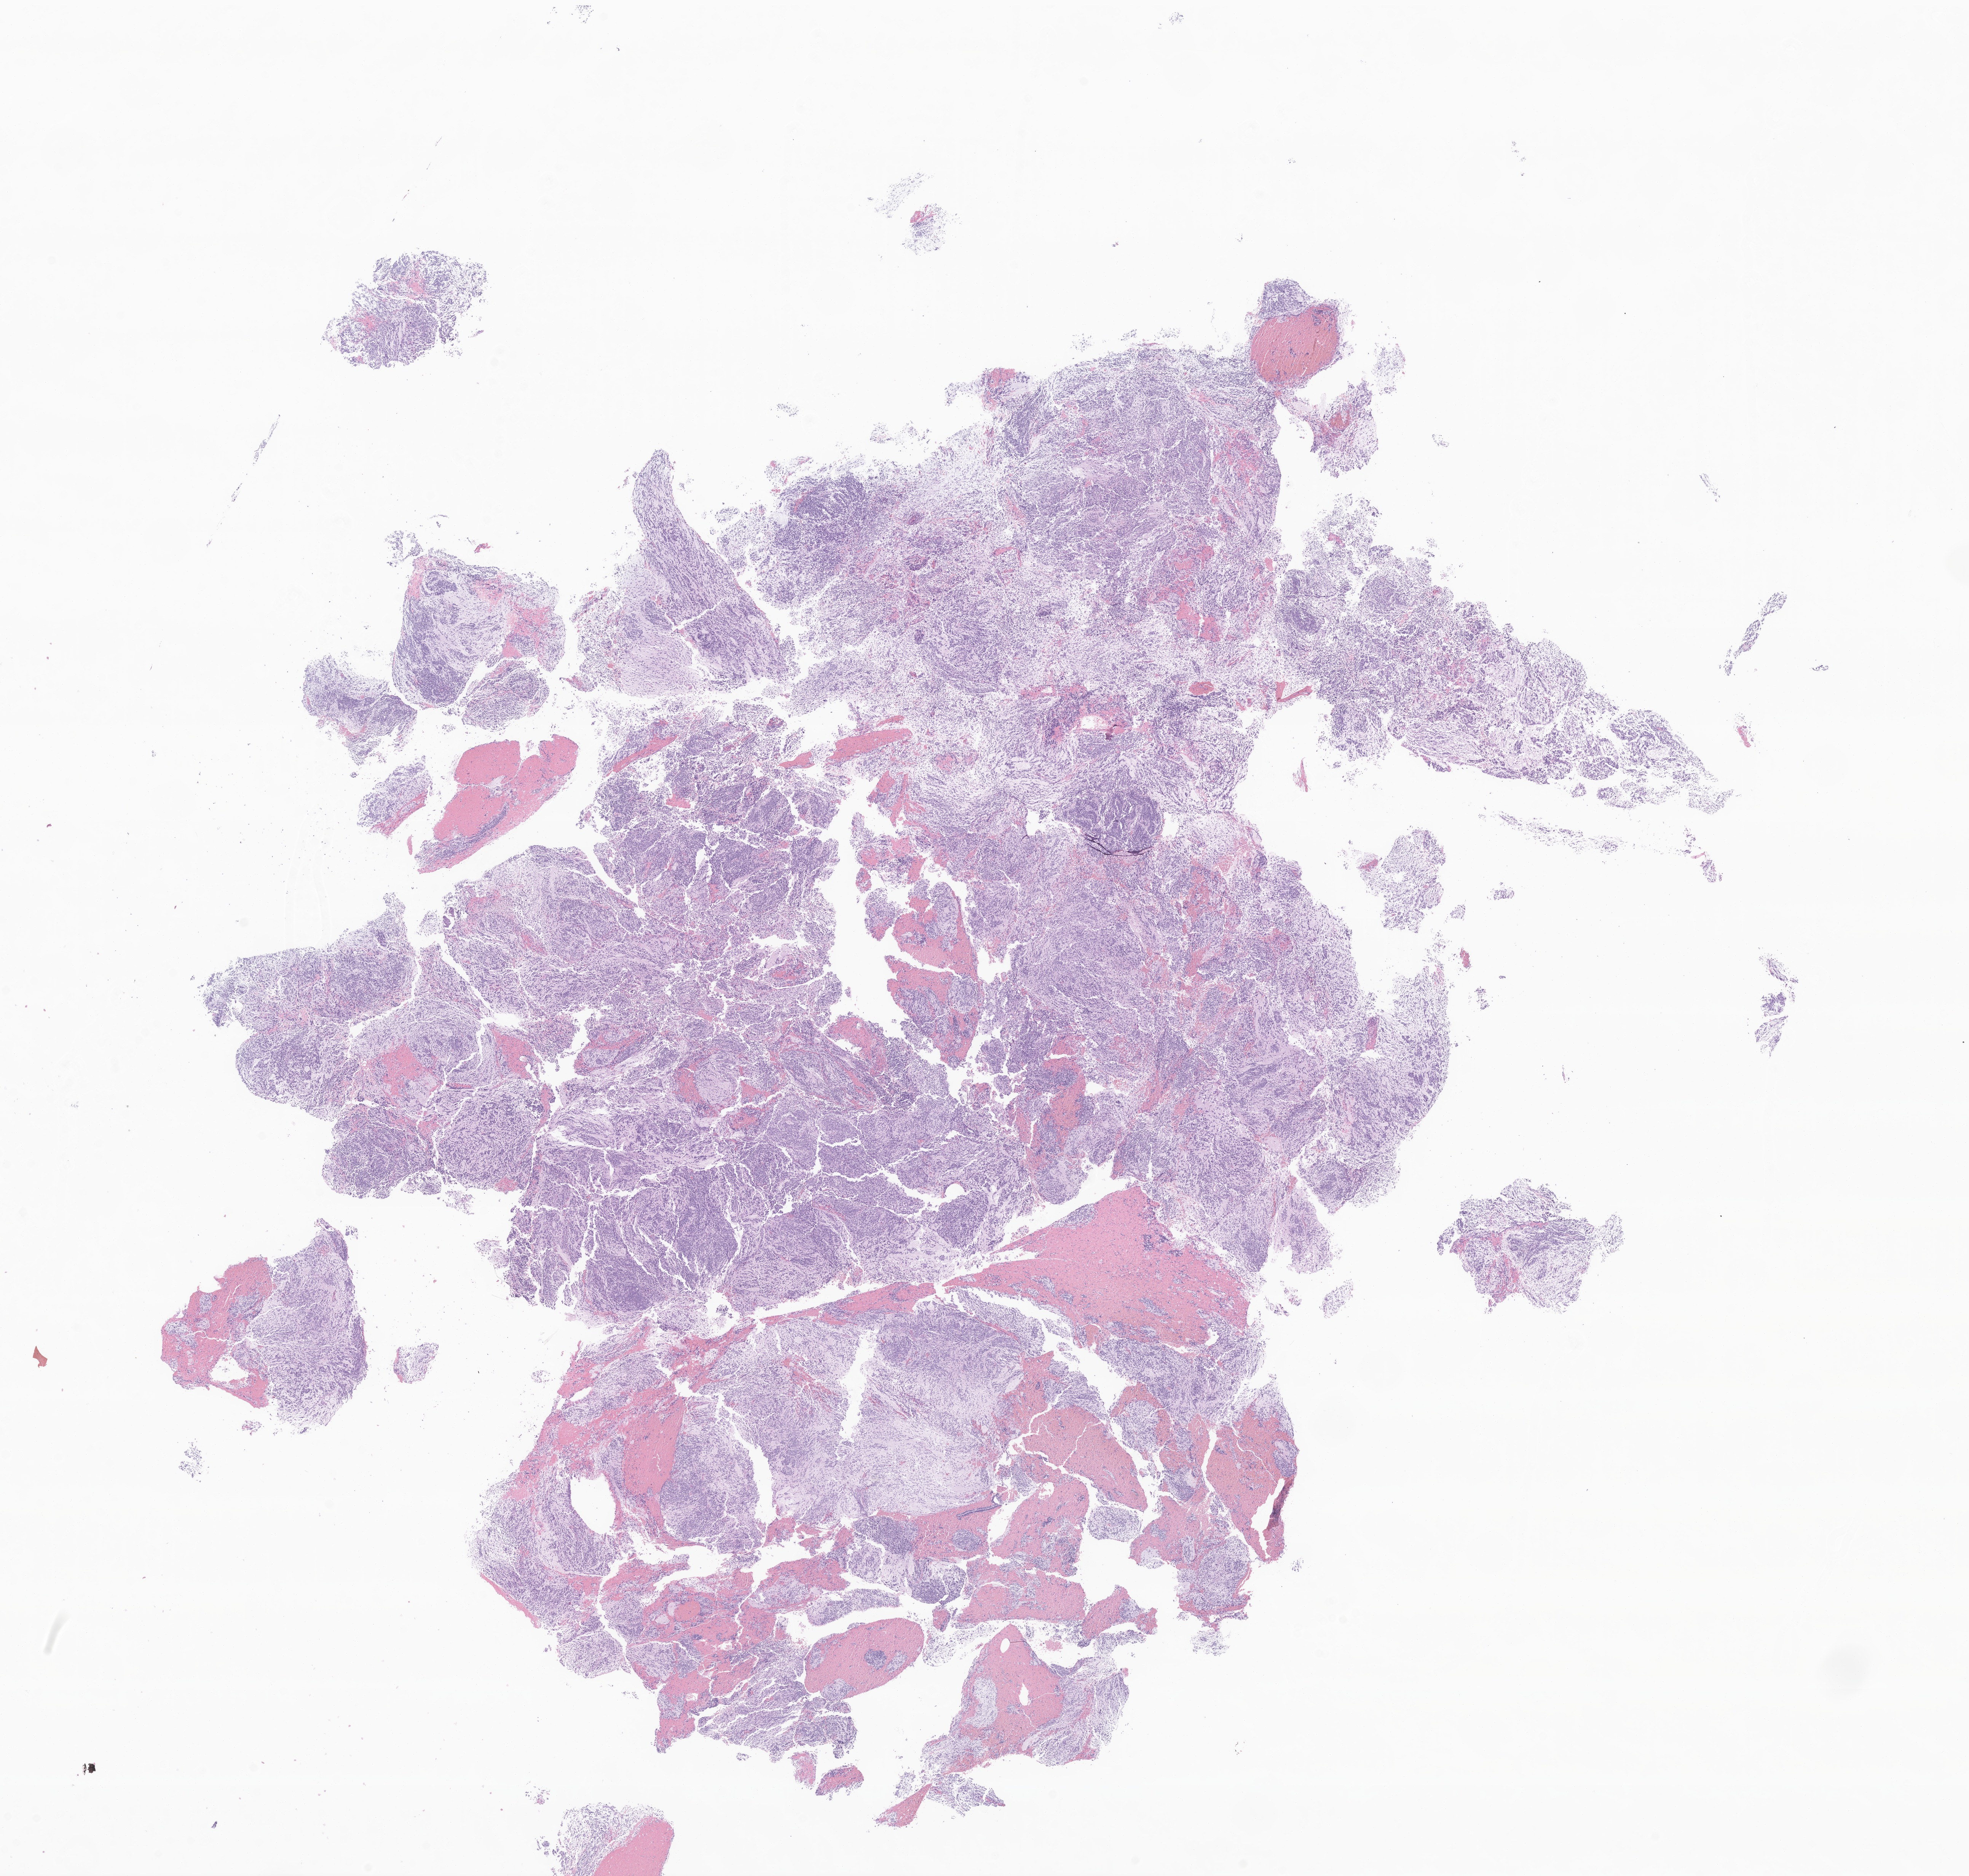
Whole-slide image, H&E stain of tumor tissue from the brain — a low-resolution overview of the entire scanned area, about 21.8 x 20.8 mm. FFPE section. Patient male; age 34 months.
• recorded diagnosis: CNS embryonal tumor, NOS